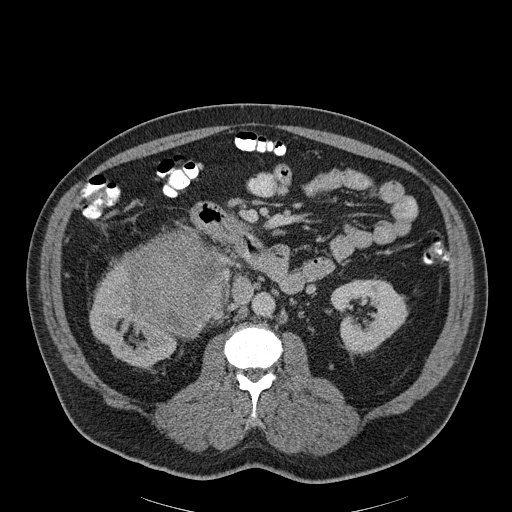
Contrast-enhanced abdominal CT, one axial slice. Position 108 of 186 along the scan axis. Soft-tissue window (W 400 / L 40 HU). 3 mm slice thickness. 512 × 512 image matrix, field of view 464 × 464 mm. Patient: male, 56 years. Case-level facts recorded for this patient, not image findings: diagnosis: adrenocortical carcinoma; tumour side: right adrenal; tumour size at pathology: 18 cm; Ki-67 index: 2 %; stage (as recorded): 3.
Structures marked on this image (semi-automatically segmented with operator editing):
- mass: box from (x=131, y=233) to (x=222, y=333) px